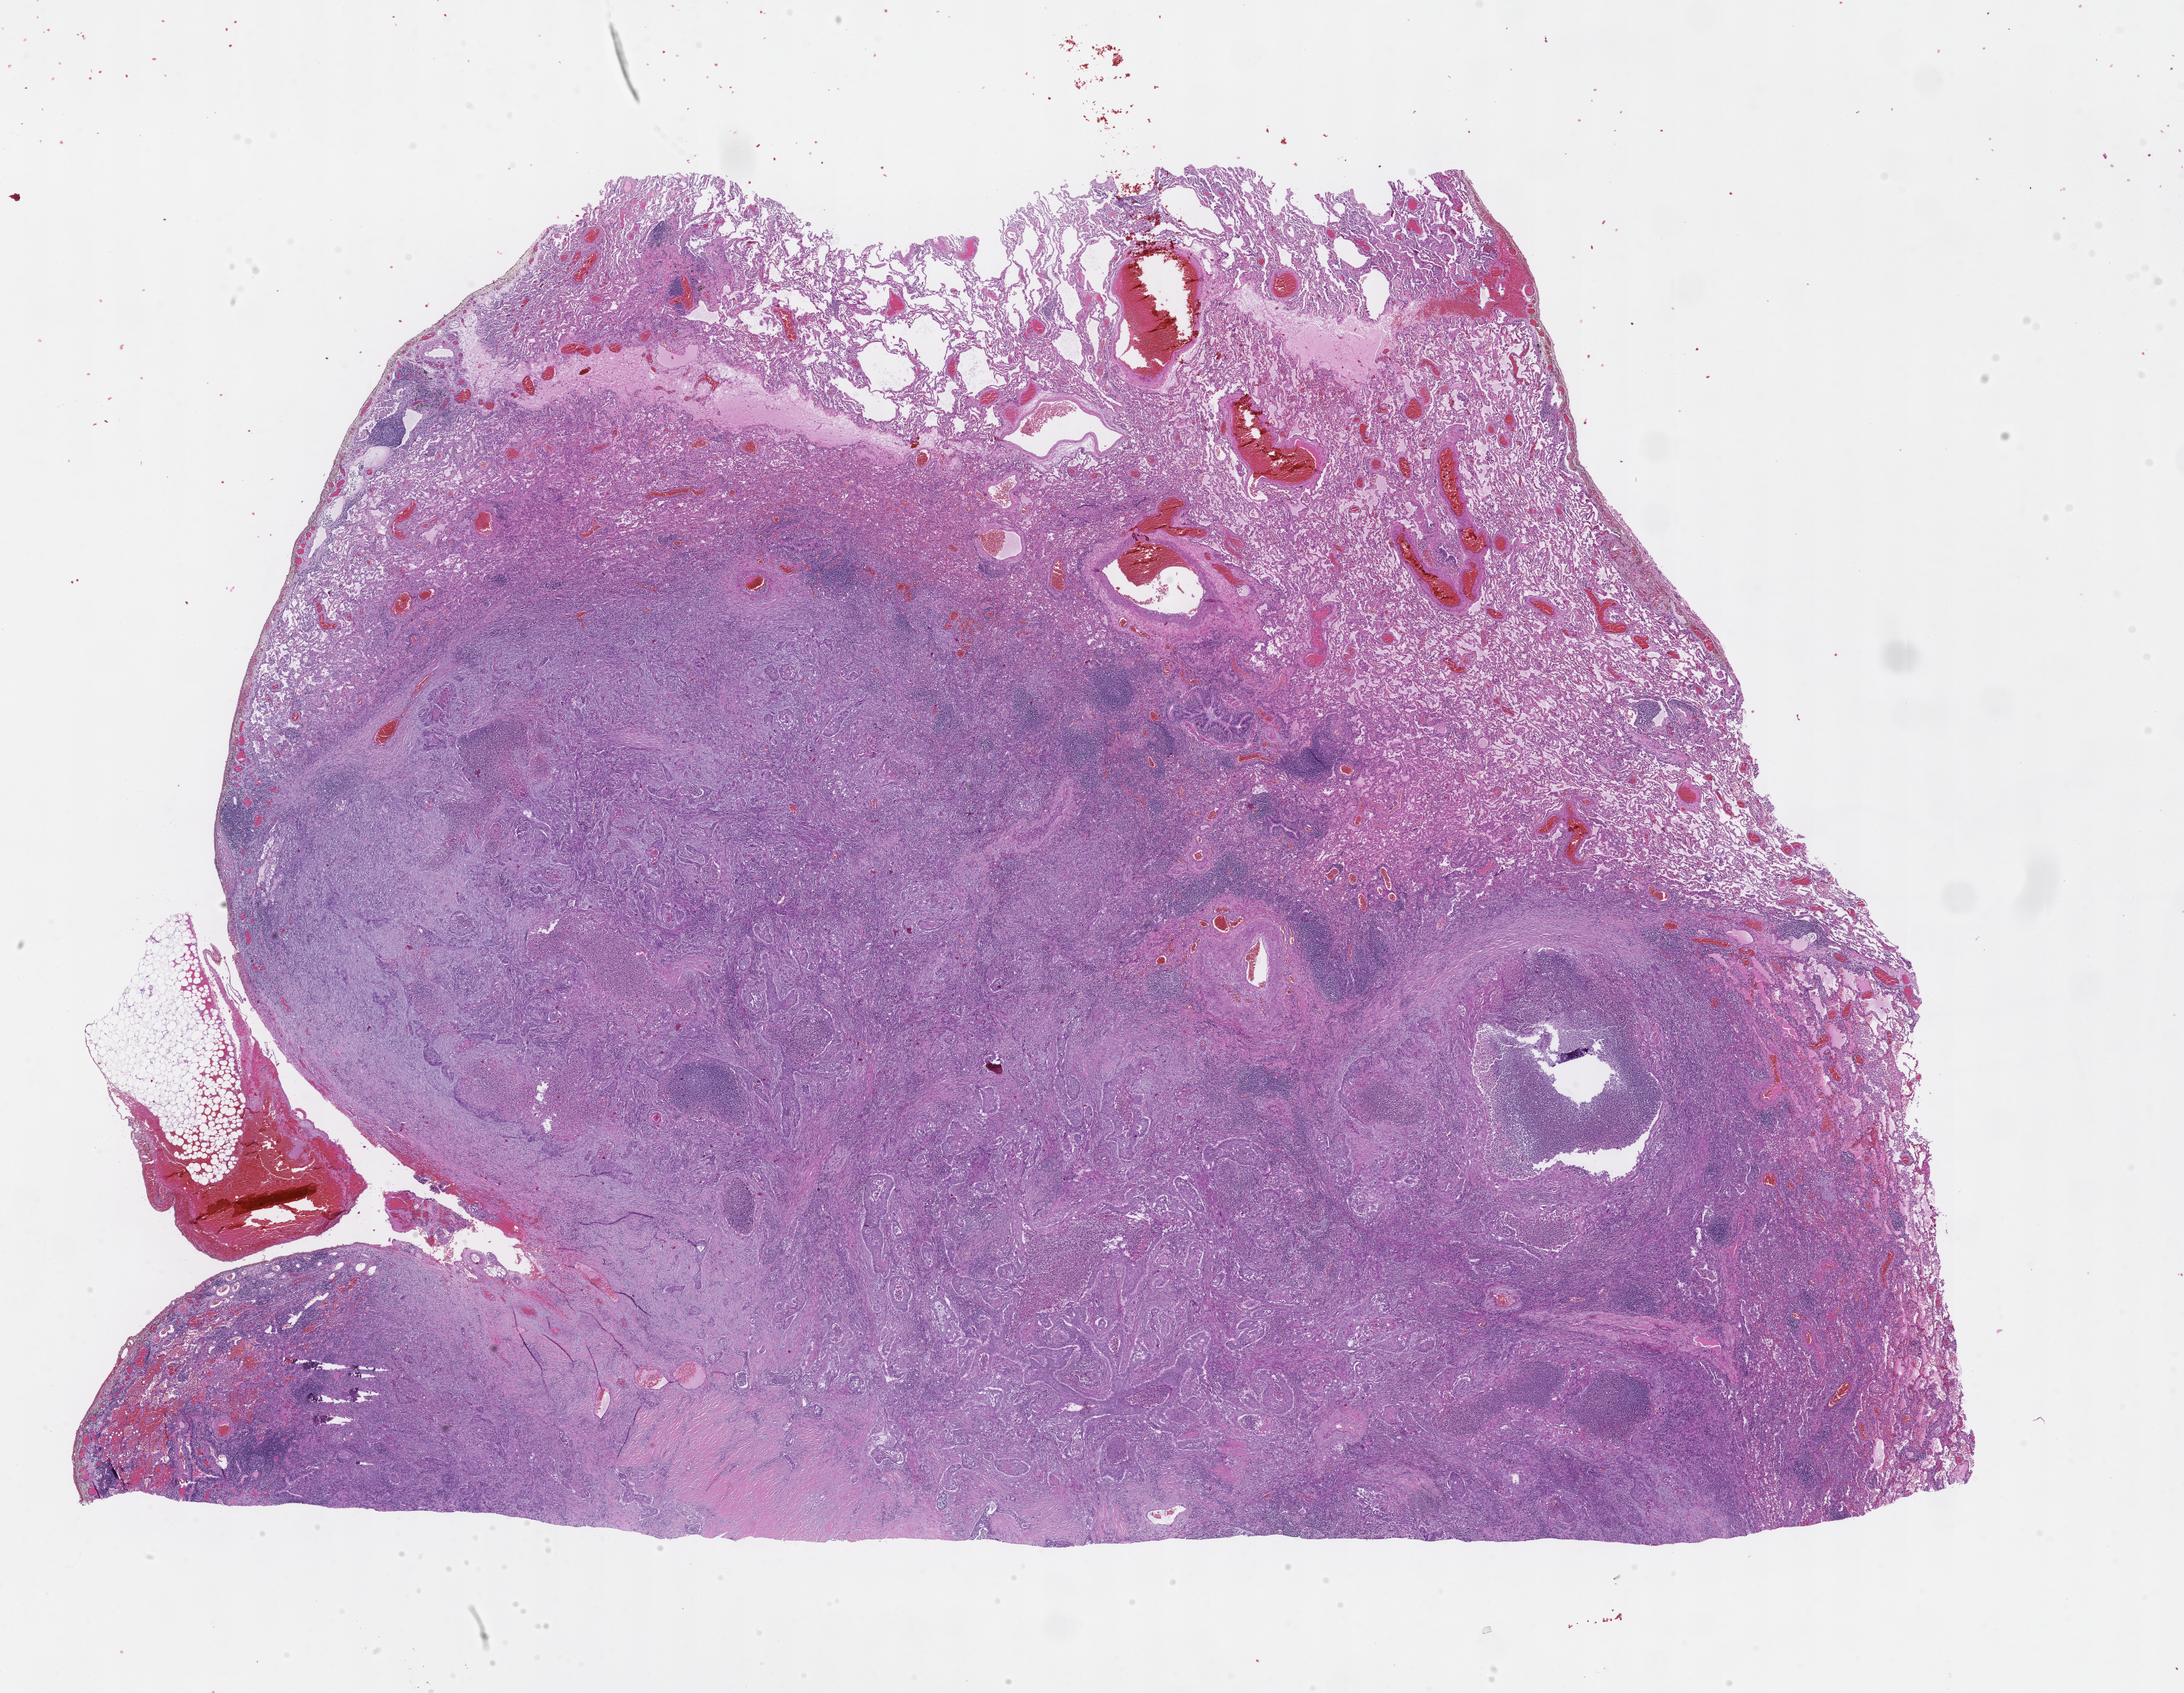
Whole-slide image, hematoxylin and eosin (H&E) stain, whole scanned area (about 23.6 x 18.3 mm) shown as a low-resolution overview; formalin-fixed, paraffin-embedded (FFPE) tissue; site: lung; specimen time point: archival tissue. Patient: female.
This section: primary tumor. Diagnosis: Non-Small Cell Lung Carcinoma.